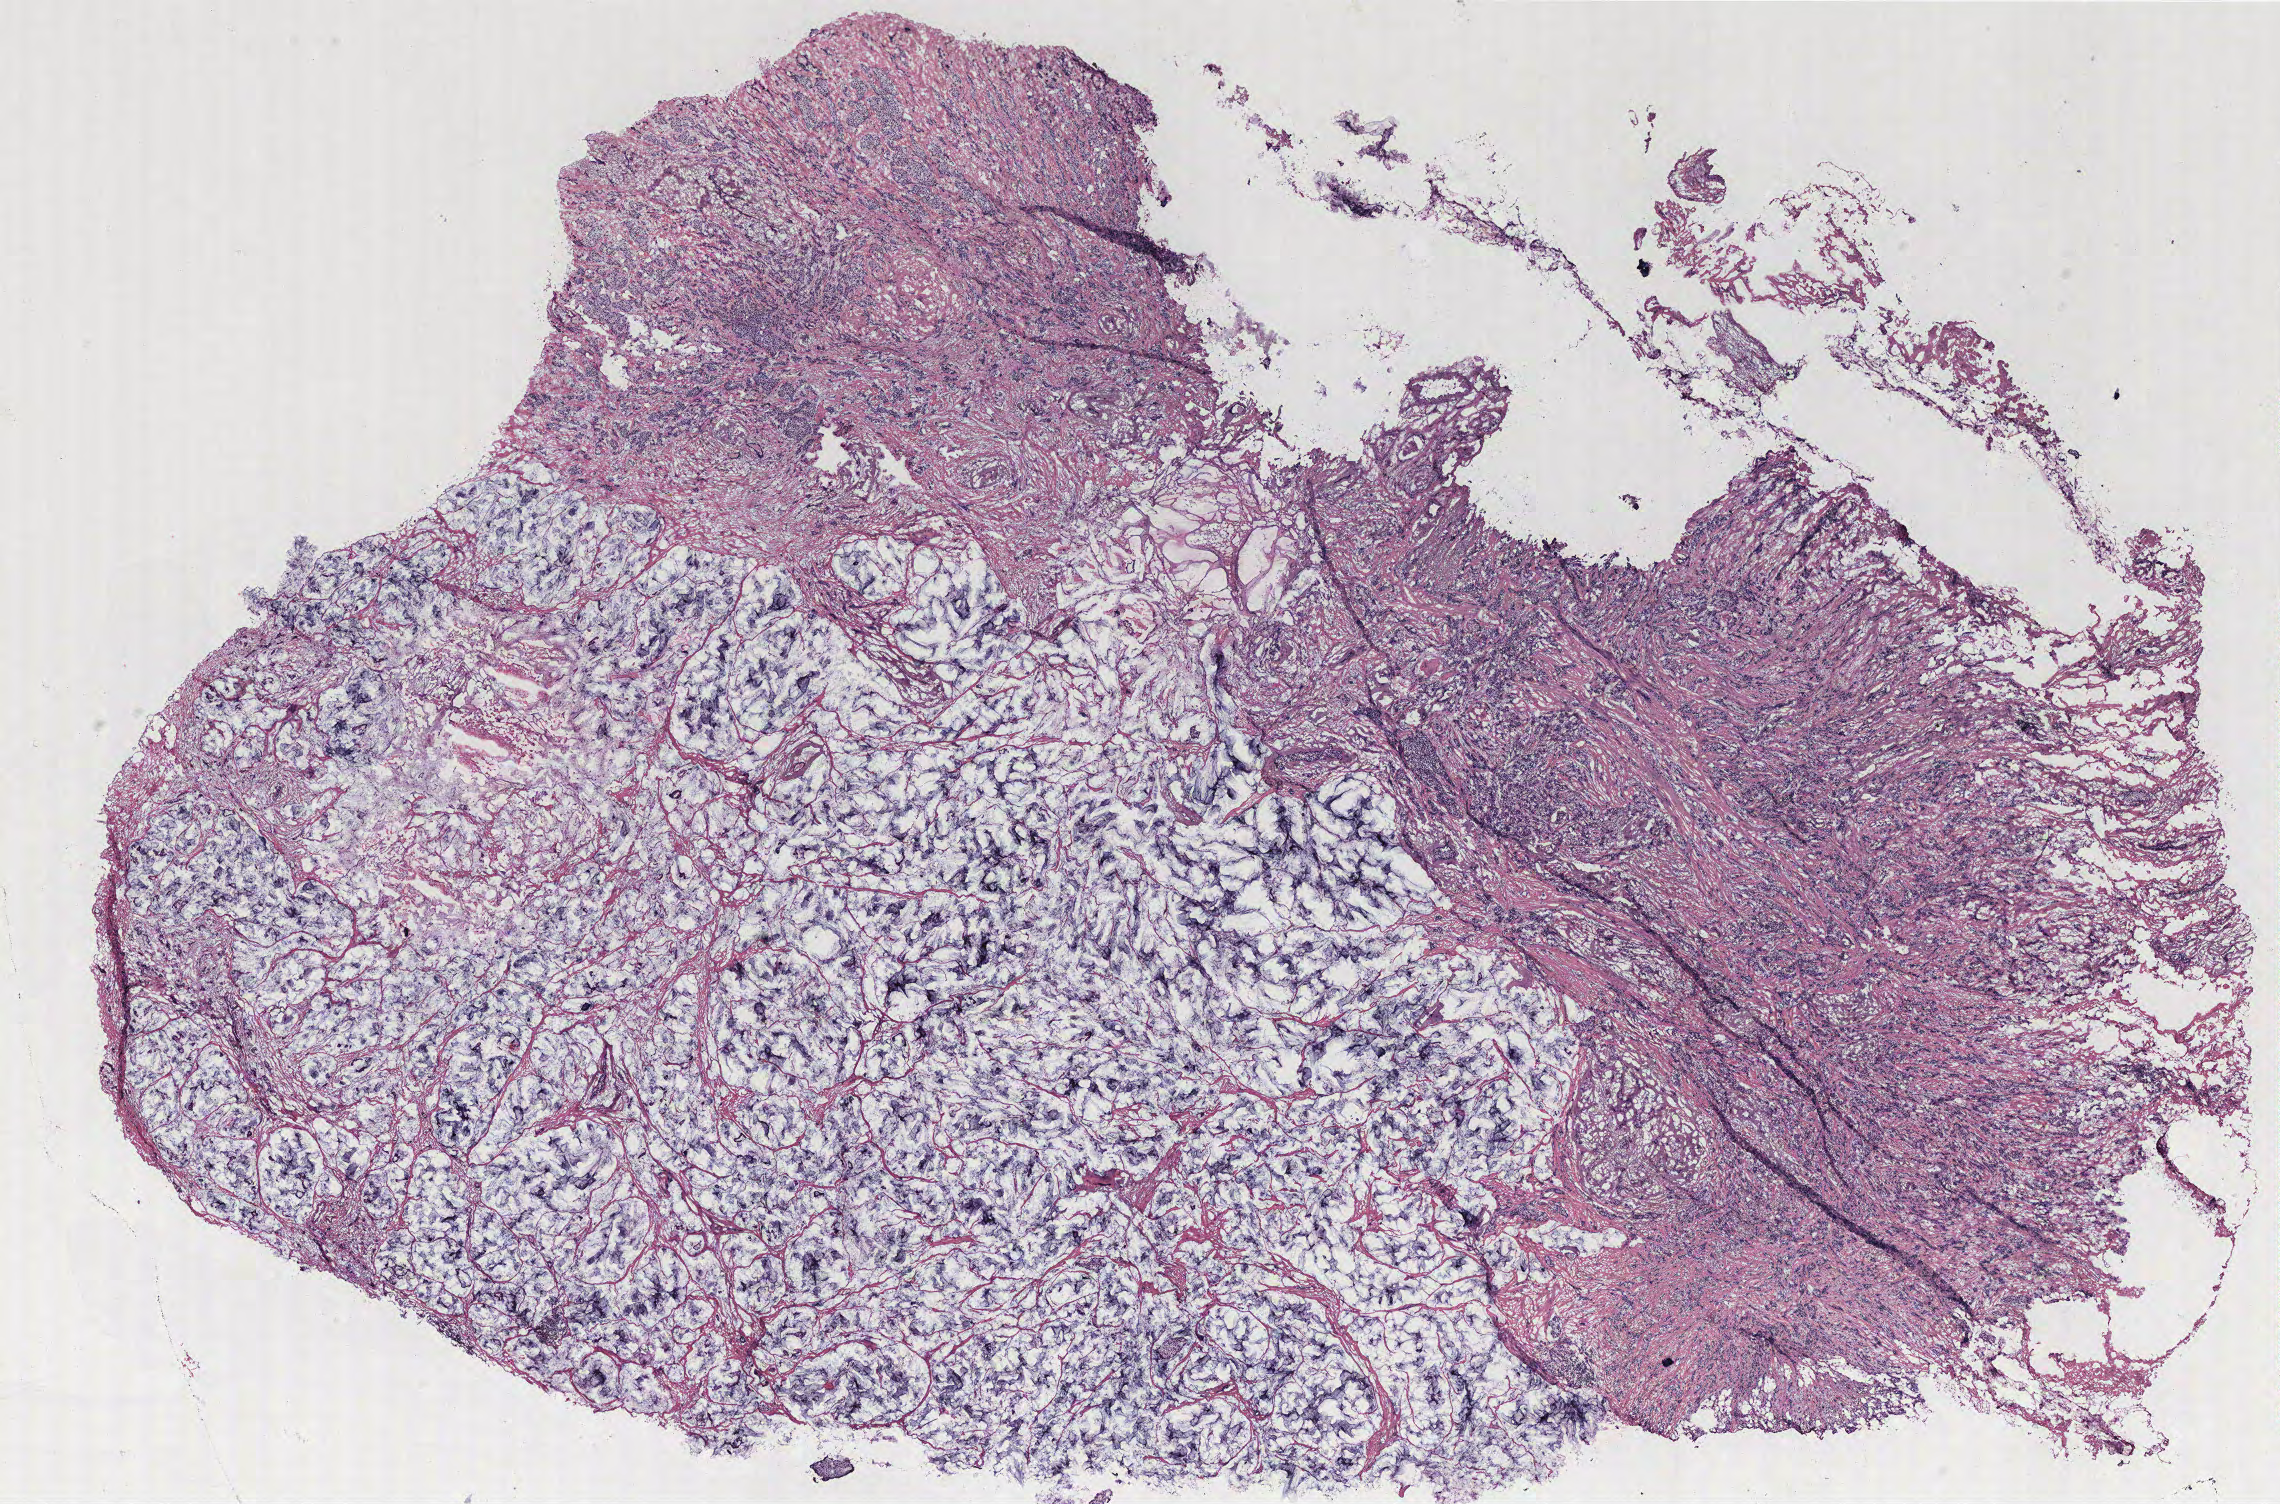
Hematoxylin and eosin (H&E) stained whole-slide image, whole scanned area (about 18.2 x 12.0 mm, from a 40x scan) shown as a low-resolution overview; breast, tissue type not recorded.
- patient diagnosis (cohort enrolment): breast cancer (breast)